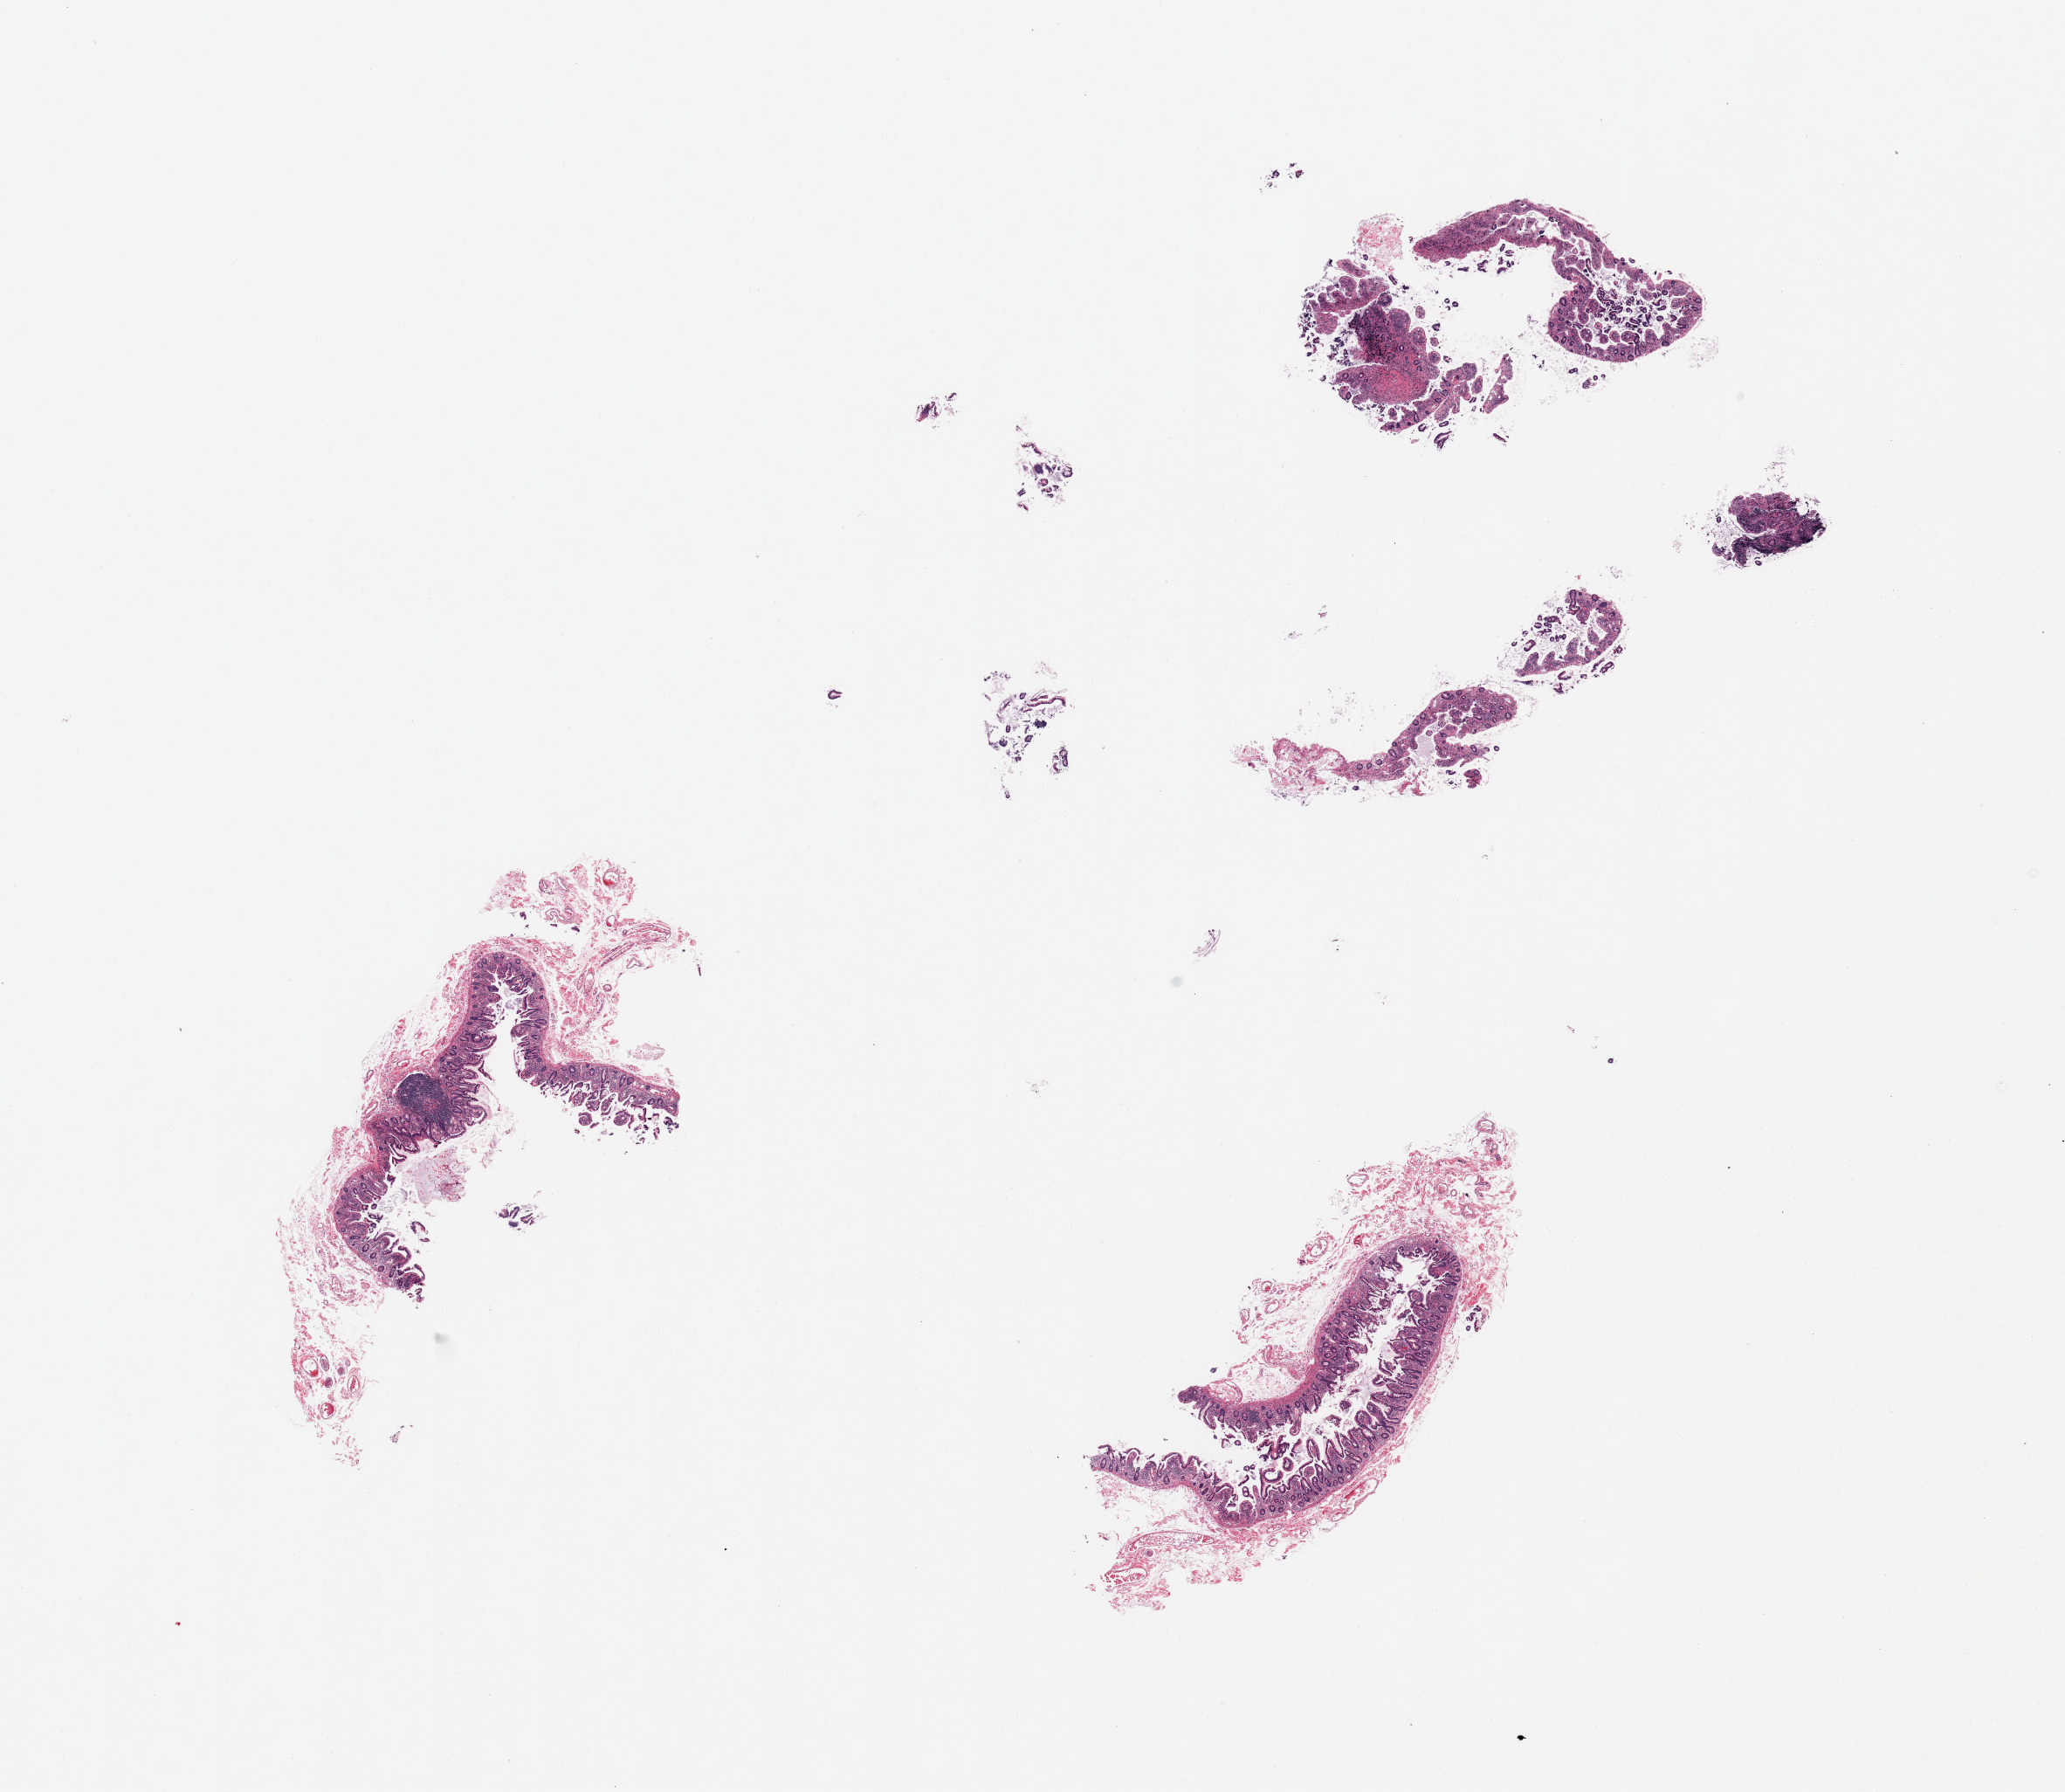
H&E whole-slide image — low-resolution overview of the scanned area, about 18.7 x 16.2 mm. Donor: female.
Specimen: PAXgene-fixed, paraffin-embedded tissue; target tissue: ileum; tissue donor sample.